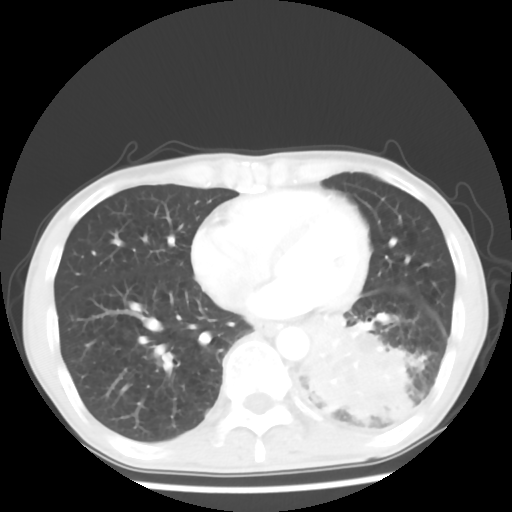
Chest CT, one axial slice; position 23 of 64 along the scan axis; 120 kVp; lung window (W 1500 / L -600 HU); 5 mm slice thickness; 512 × 512 image matrix. Patient: male, 68 years. From the clinical record (not read from this slice): clinical TNM (as recorded): T4 N0 M0.
Structures marked on this image (bounding box drawn by a radiologist):
- lung tumour (recorded histology: squamous cell carcinoma): bounding box <304,309,432,449> (left, top, right, bottom; pixels)